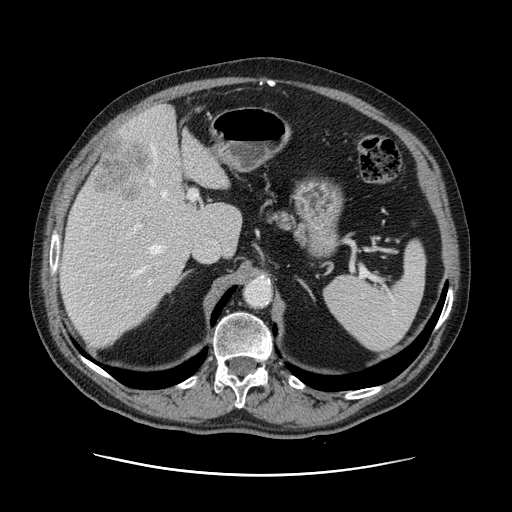
Contrast-enhanced abdominal CT, one axial slice; 120 kVp; soft-tissue window (W 400 / L 40 HU); 512 × 512 image matrix. Male patient, age 72 years. Case-level facts recorded for this patient, not image findings: diagnosis: colorectal cancer liver metastases, imaged before liver resection; multiple liver metastases: yes; largest metastasis: 5.4 cm.
Outlined on this slice (outlined manually by an expert reader):
- hepatic veins: bounding box (x1, y1, x2, y2) in pixels: (134, 146, 167, 275)
- liver: (60, 105, 242, 347)
- planned liver remnant (the part of the liver to remain after resection): (60, 130, 242, 346)
- portal vein (with intrahepatic branches): (93, 190, 198, 282)
- liver metastasis: (95, 140, 153, 201)